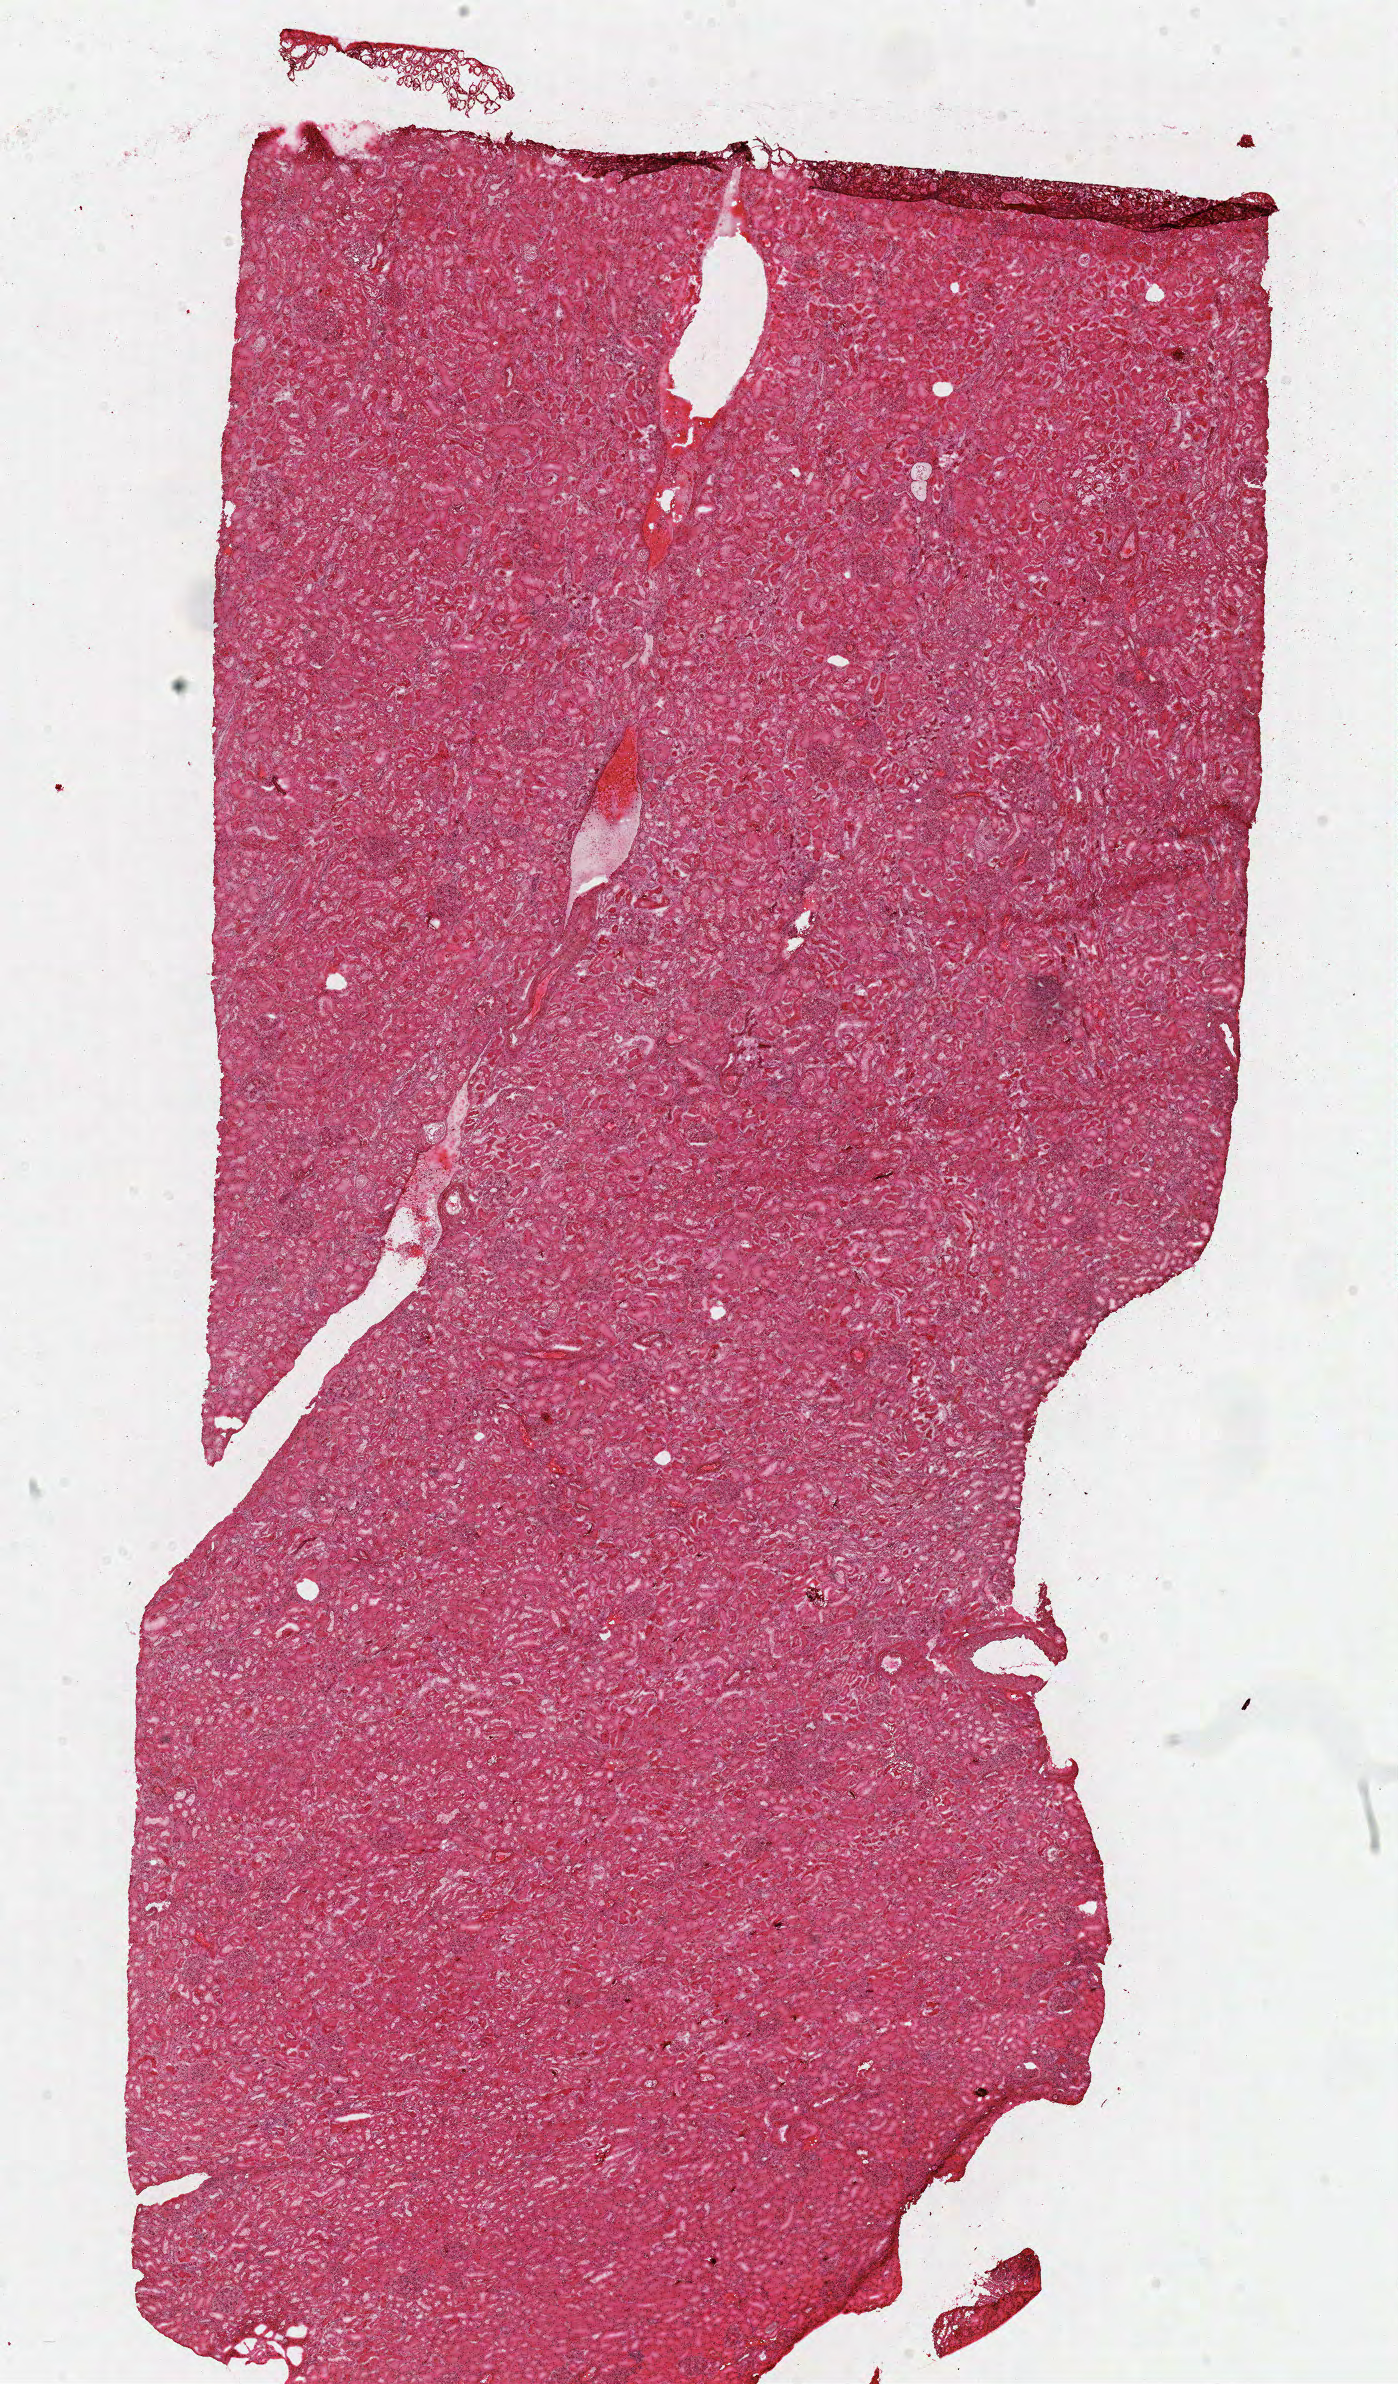
Digitized H&E-stained tissue section (whole slide), whole scanned area (about 11.0 x 18.8 mm, slide scanned at 40x) shown as a low-resolution overview, frozen section, sample: solid tissue normal (non-tumour tissue), kidney. Male patient; age at initial diagnosis 60 years.
This section: solid tissue normal (non-tumour) sample from the same patient. Patient diagnosis: Papillary adenocarcinoma, NOS.